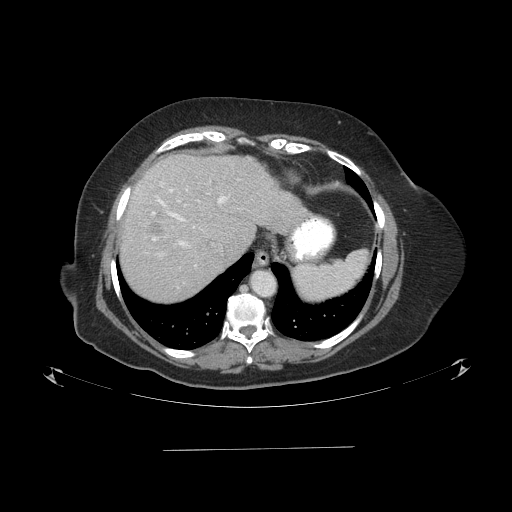
Contrast-enhanced abdominal CT (liver protocol), one axial slice; slice 73 of 103 in the series (ordered by position); one of 2 acquisitions stored at this slice position; soft-tissue window (W 400 / L 40 HU); 2.5 mm slice thickness; 512 × 512 image matrix, field of view 500 × 500 mm. Case-level facts recorded for this patient, not image findings: diagnosis: hepatocellular carcinoma (patient treated with transarterial chemoembolisation; whether this scan precedes or follows treatment is not stated here); TNM stage (as recorded): Stage-IIIA; Child-Pugh class: A; tumour differentiation: poorly differentiated; tumour size: 5.2 cm.
Annotated regions visible in this slice (semi-automatically segmented with operator editing):
- liver parenchyma outside the tumour (the mass and vessels are separate outlines, so this box may not span the whole liver): bounding box (x1, y1, x2, y2) in pixels: (118, 152, 308, 300)
- mass: (144, 218, 166, 238)
- liver vessels: (152, 182, 228, 266)